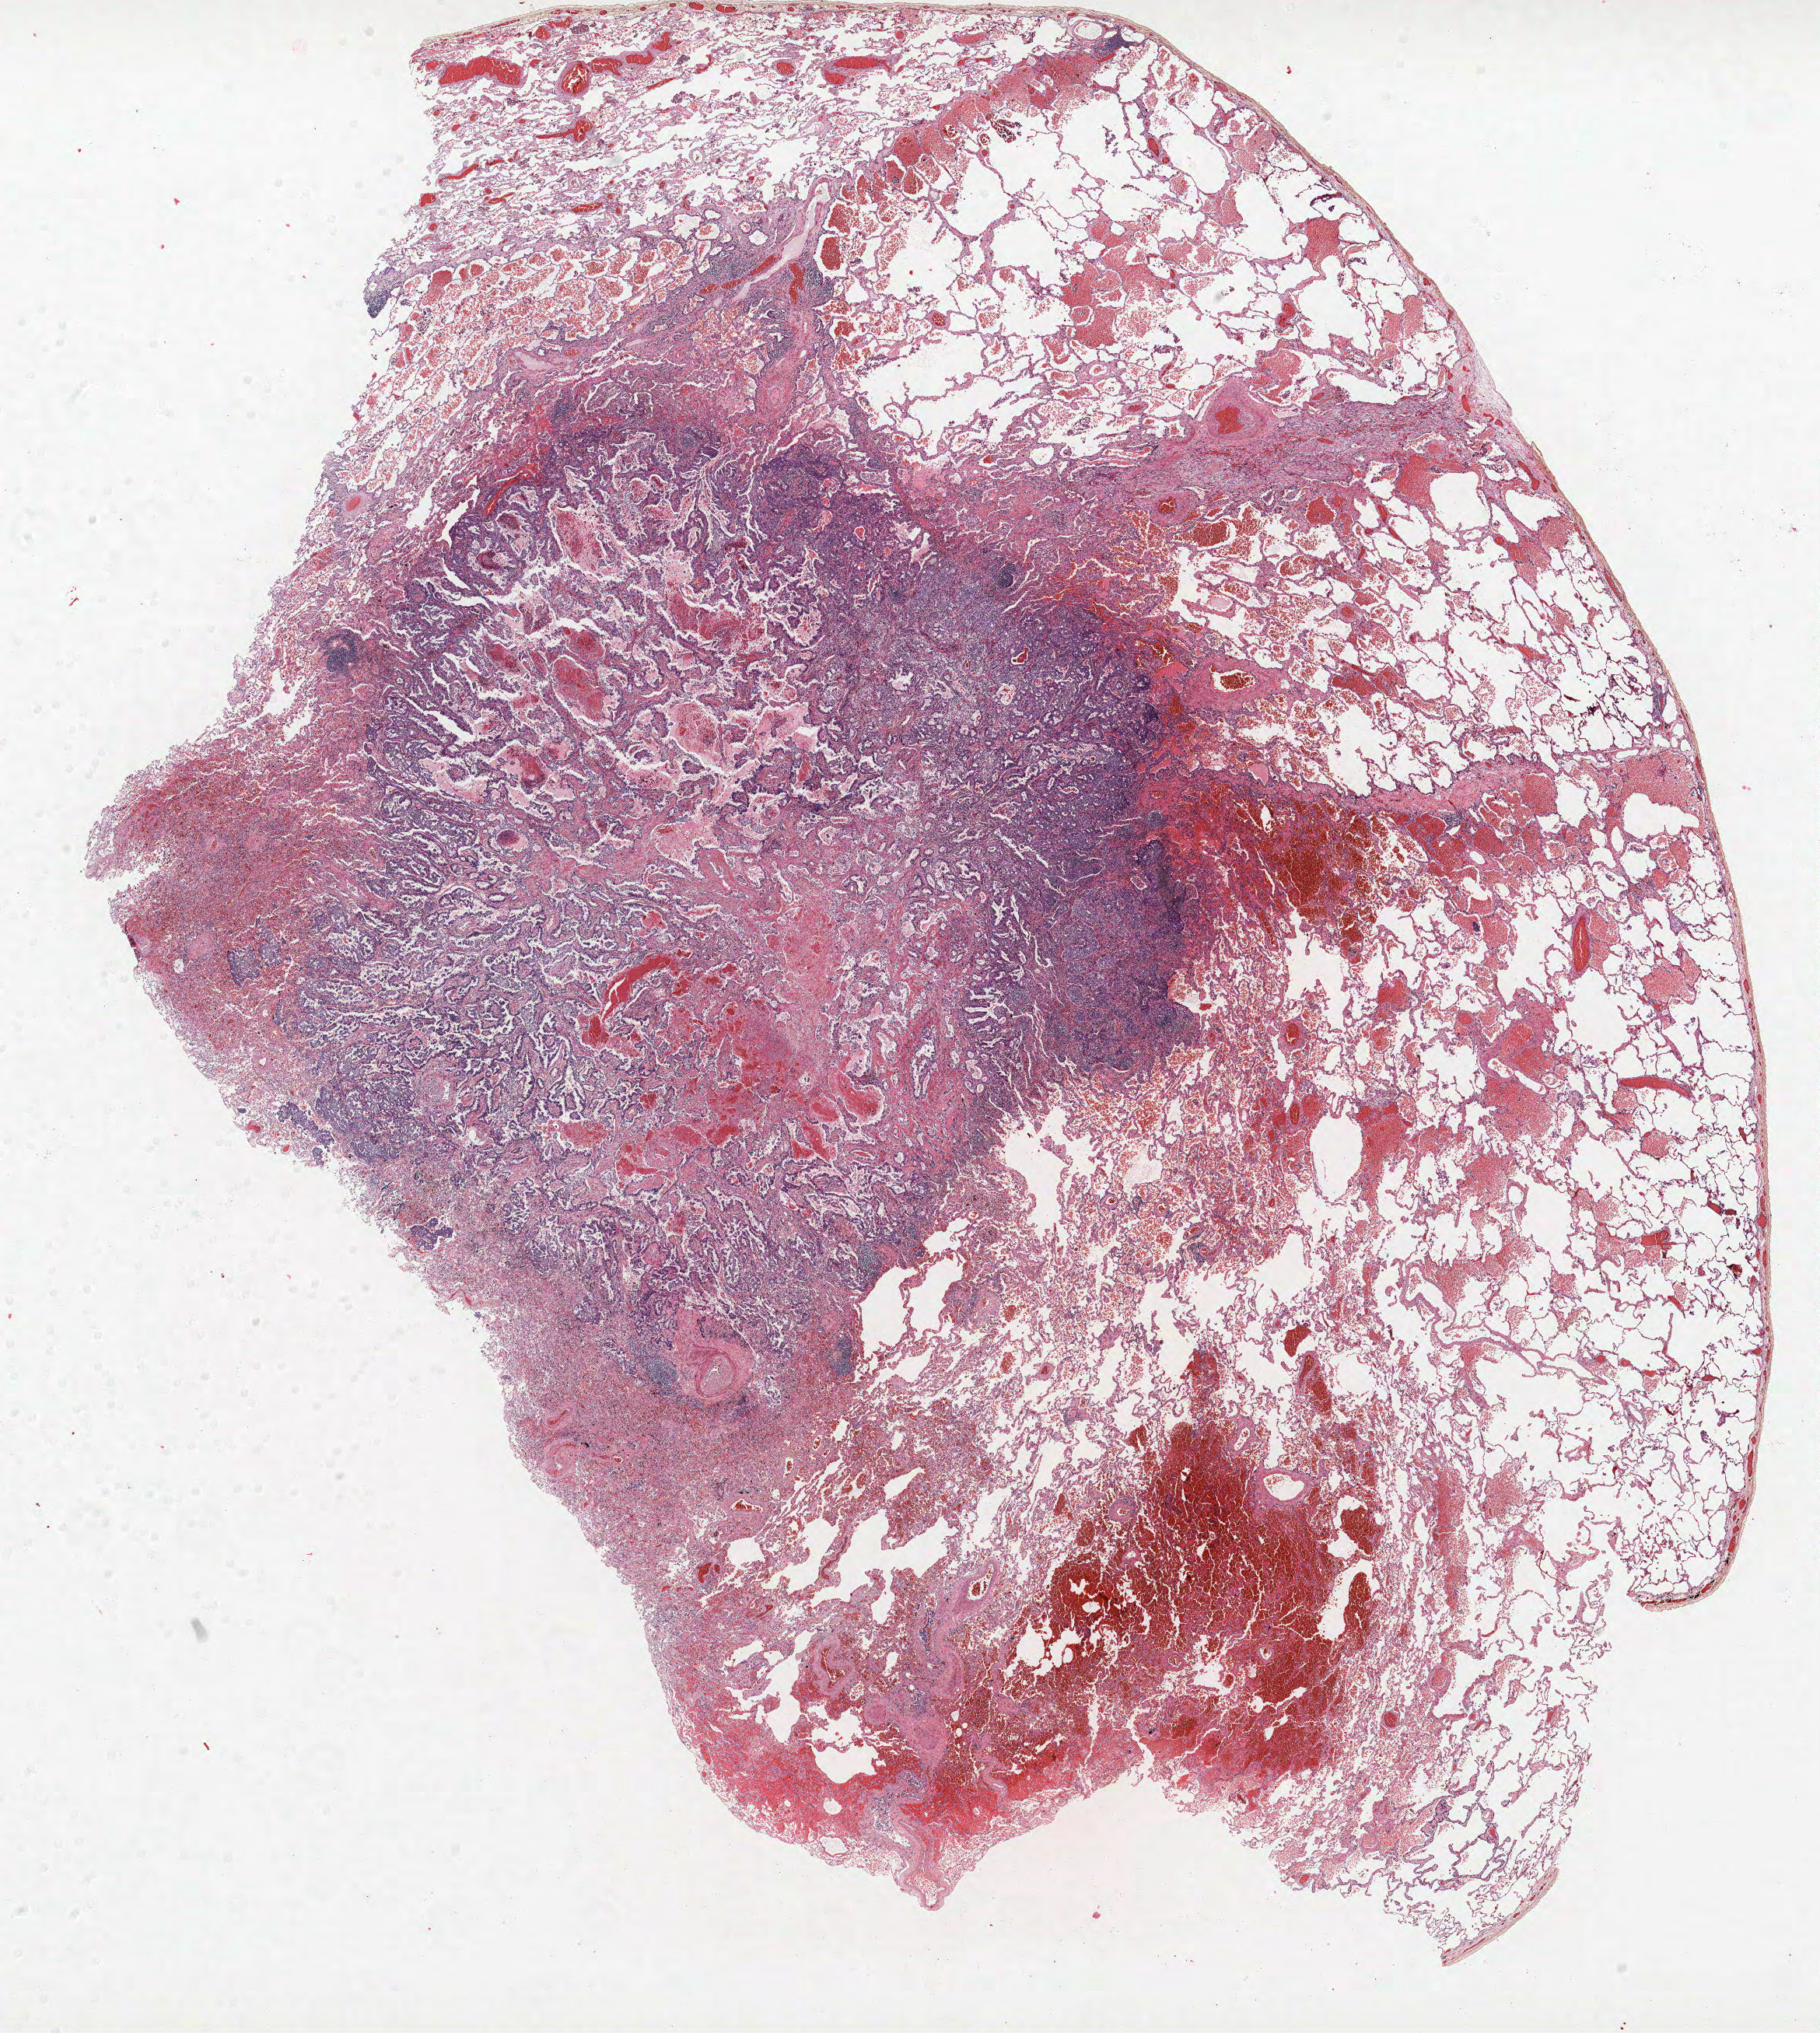
H&E whole-slide image — low-resolution overview of the scanned area, about 18.7 x 20.9 mm, formalin-fixed paraffin-embedded (FFPE) section, lung. Male, age 63 at enrolment. Current smoker at enrolment. Grade: moderately differentiated (G2).
ICD-O-3 topography: lower lobe of lung (C34.3). Participant's lung-cancer diagnosis: Adenocarcinoma, NOS. Tumour size (pathology): 12 mm. Primary tumour location (clinical record): right lower lobe. Stage (AJCC 6th edition): IA. Note: participant had 3 primary lung cancers recorded; fields above describe the first.